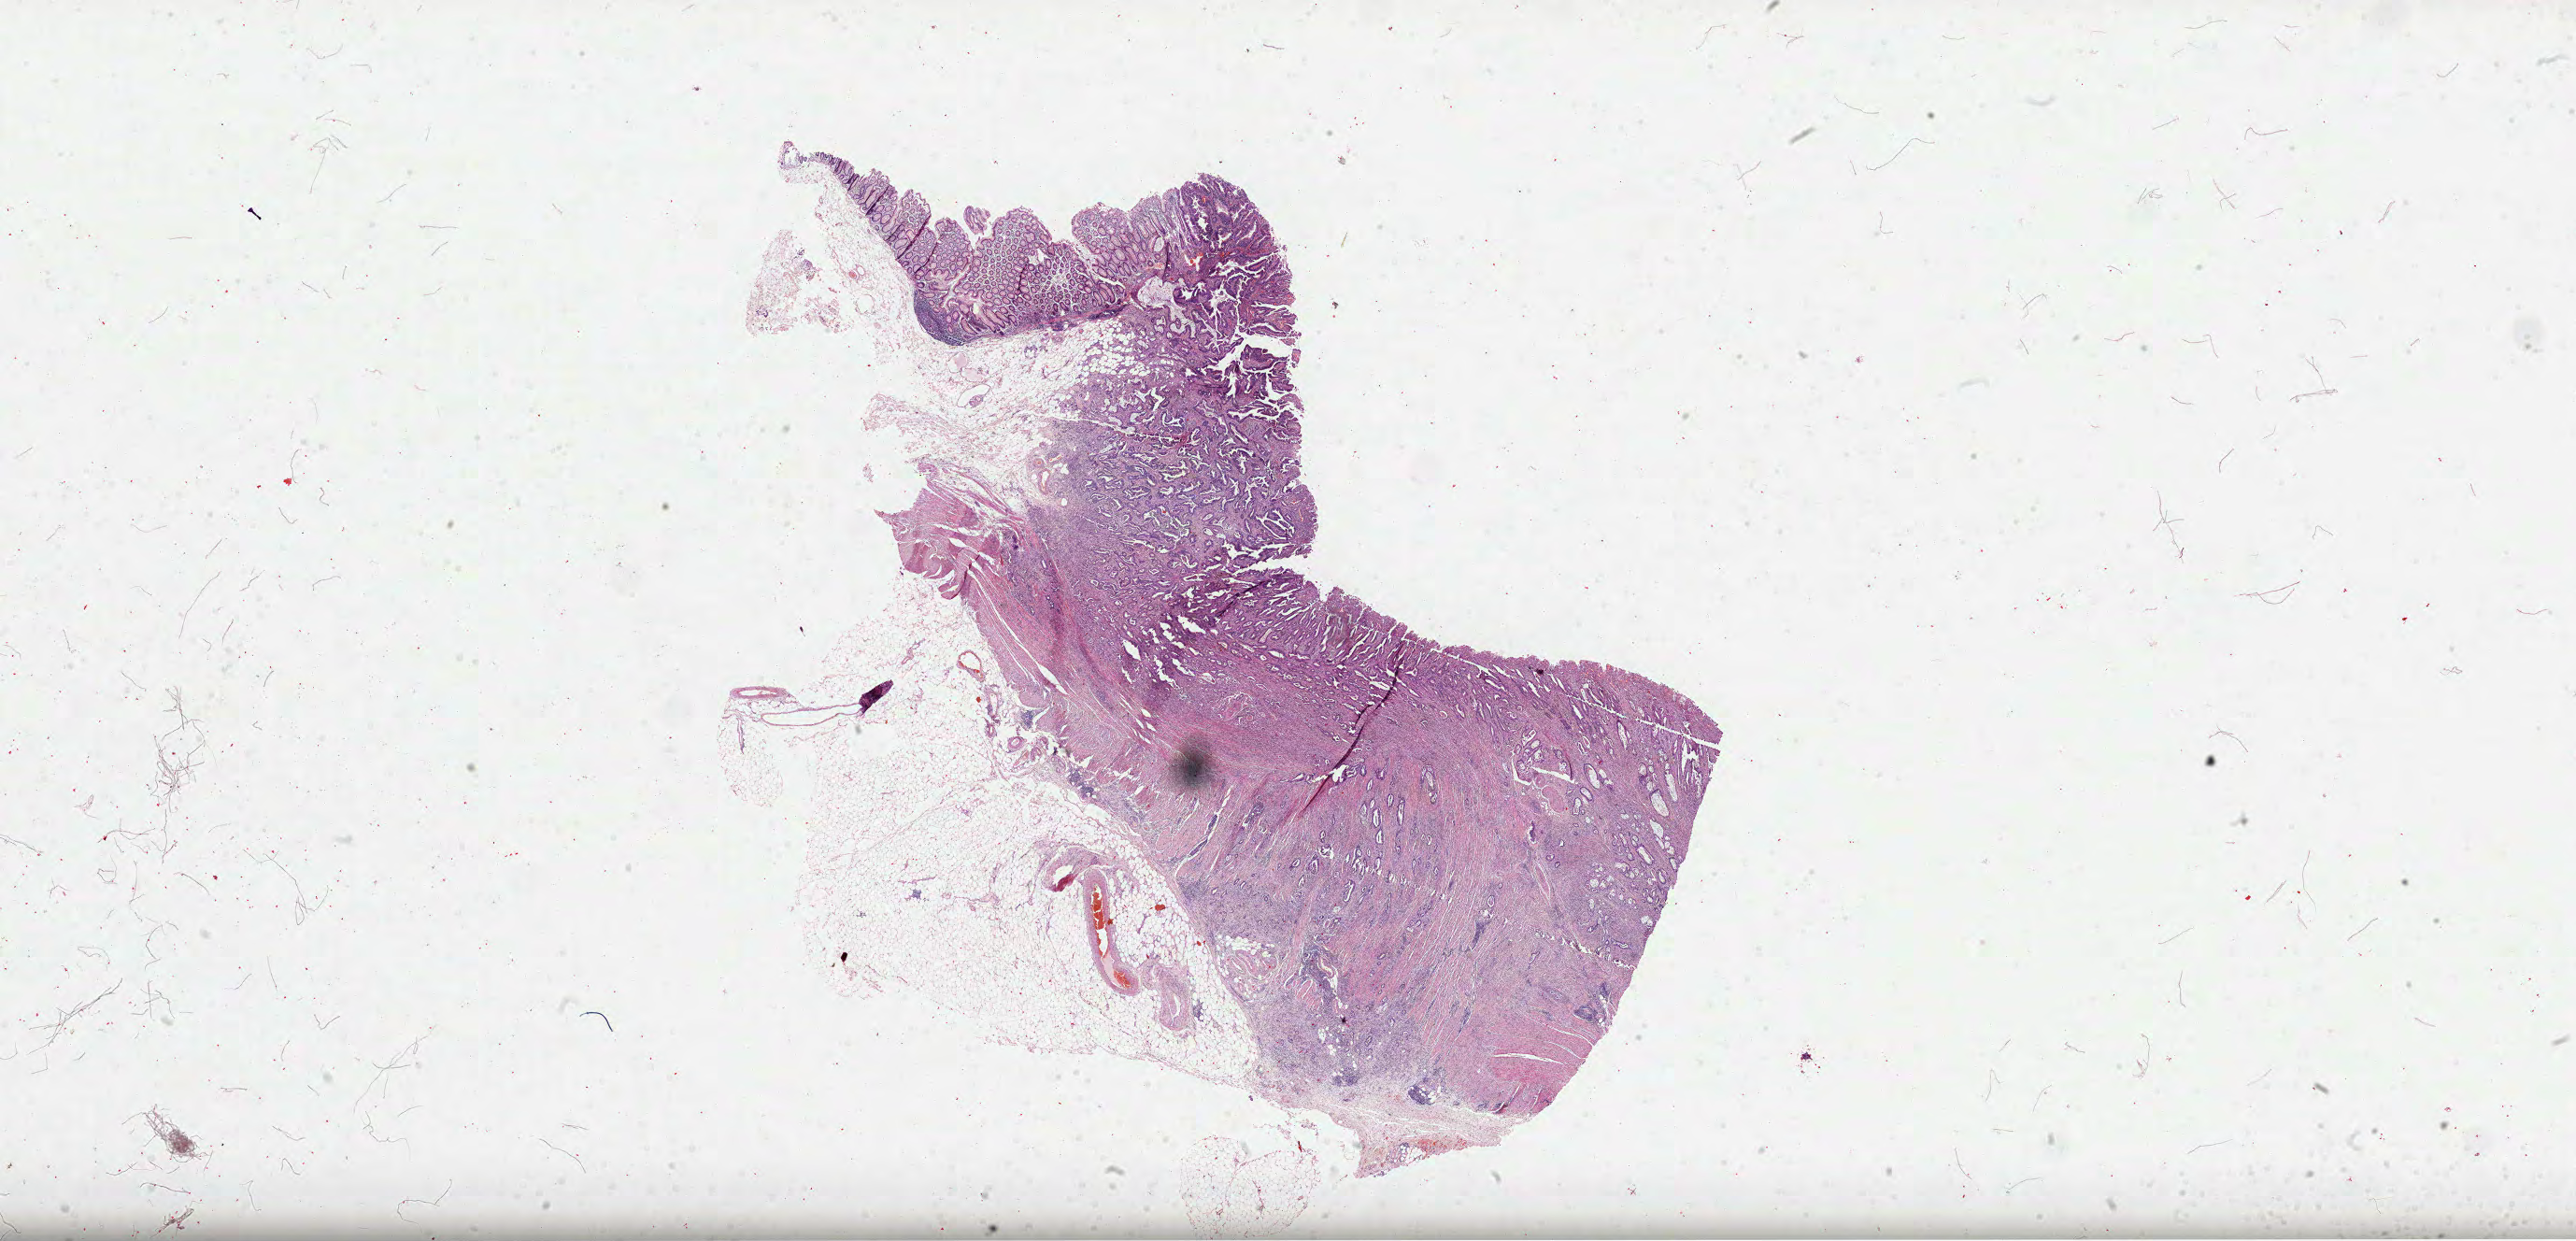
Digitized H&E tissue section (whole slide), whole scanned area (about 44.5 x 21.4 mm, from a 40x scan) shown as a low-resolution overview, formalin-fixed paraffin-embedded (FFPE) diagnostic section, colon, primary tumour sample. Male patient; age at initial diagnosis 60 years.
Lymph nodes positive (case pathology): 1 of 4 examined. AJCC pathologic stage: IIIA. Pathologic diagnosis: Mucinous adenocarcinoma (ascending colon).